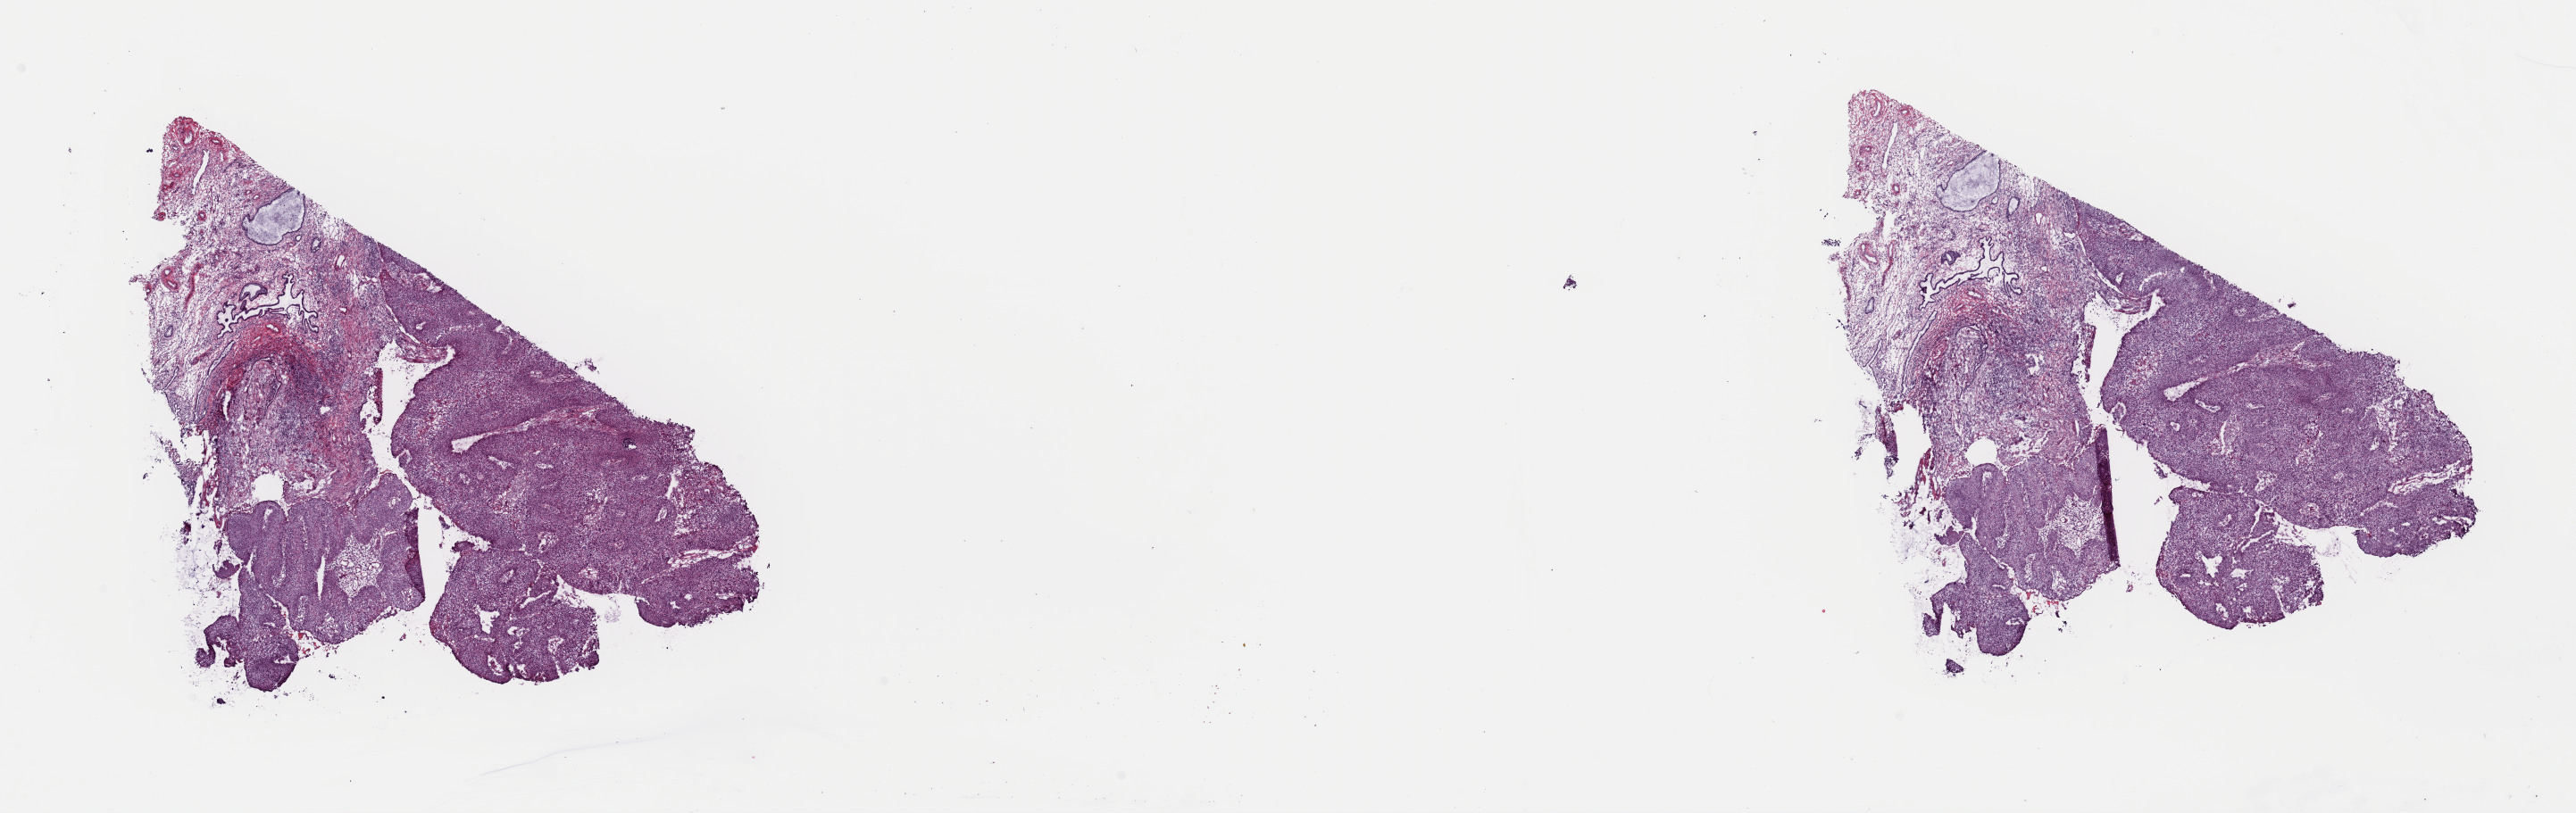
Hematoxylin and eosin (H&E) stained whole-slide image, low-resolution overview of the scanned area, about 22.8 x 7.2 mm (from a 40x scan). Frozen section from the top of the tissue portion. Primary tumour sample from the cervix. Female patient; age at initial diagnosis 40 years. Histologic grade: G3 (poorly differentiated). Slide review estimates, as recorded: tumour cells 70%, tumour nuclei 70%, normal cells 0%, stromal cells 30%, necrosis 0%. Inflammatory infiltration, as recorded: lymphocyte infiltration 20%, monocyte infiltration 20%, neutrophil infiltration 40%.
• FIGO stage: IB1
• diagnosis: Squamous cell carcinoma, large cell, nonkeratinizing, NOS (cervix uteri)